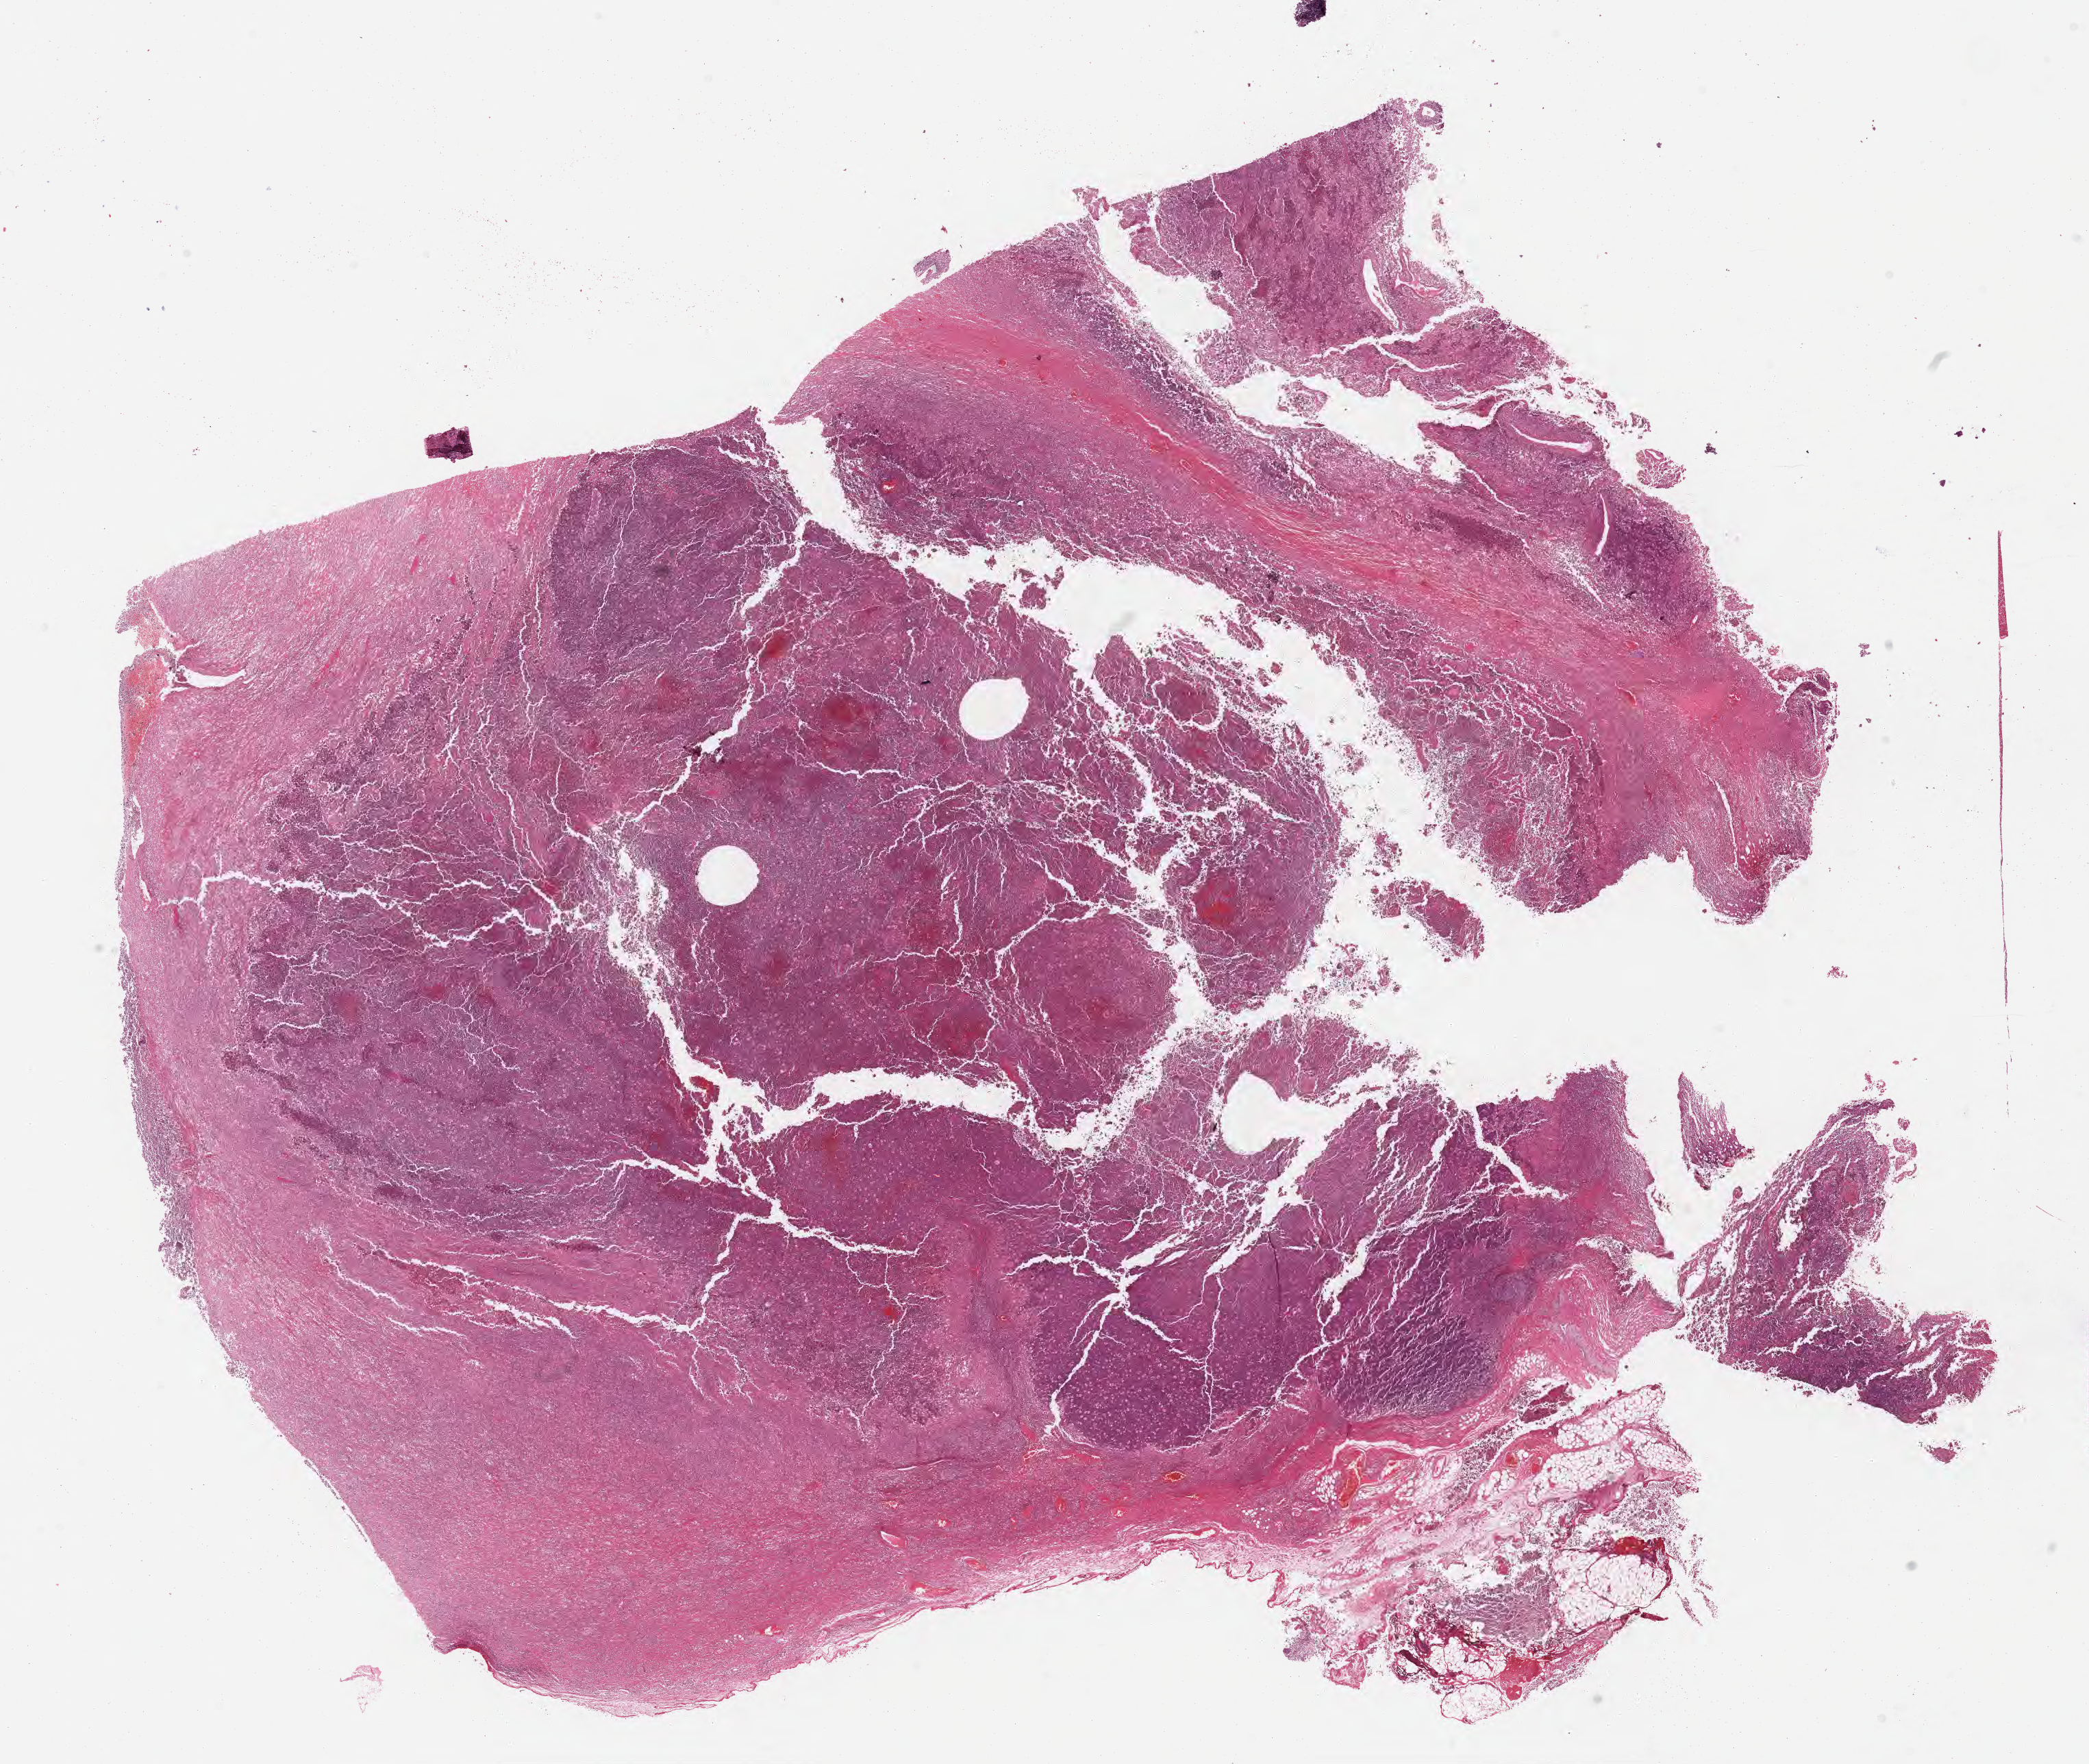
Whole-slide image, H&E stain, shown as a low-resolution overview of the whole scanned area (about 24.6 x 20.8 mm); formalin-fixed paraffin-embedded section; primary tumor. Female patient, aged 74.
Histologic diagnosis: Burkitt lymphoma, NOS.